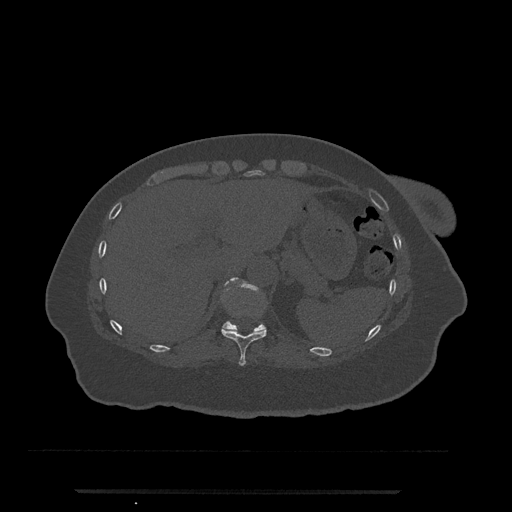
CT including the spine, one axial slice. Position 266 of 797 along the scan axis. 120 kVp. Bone window (W 1800 / L 400 HU). 512 × 512 image matrix, field of view 440 × 440 mm. Female patient, age 51 years. From the clinical record (not read from this slice): primary cancer: neuro; vertebrae with lytic lesions (as recorded): T8.
Outlined on this slice (semi-automatic segmentation, software-assisted and operator-edited):
- T10 vertebra: bounding box <221,327,267,366> (left, top, right, bottom; pixels)
- T11 vertebra: <222,281,265,331>